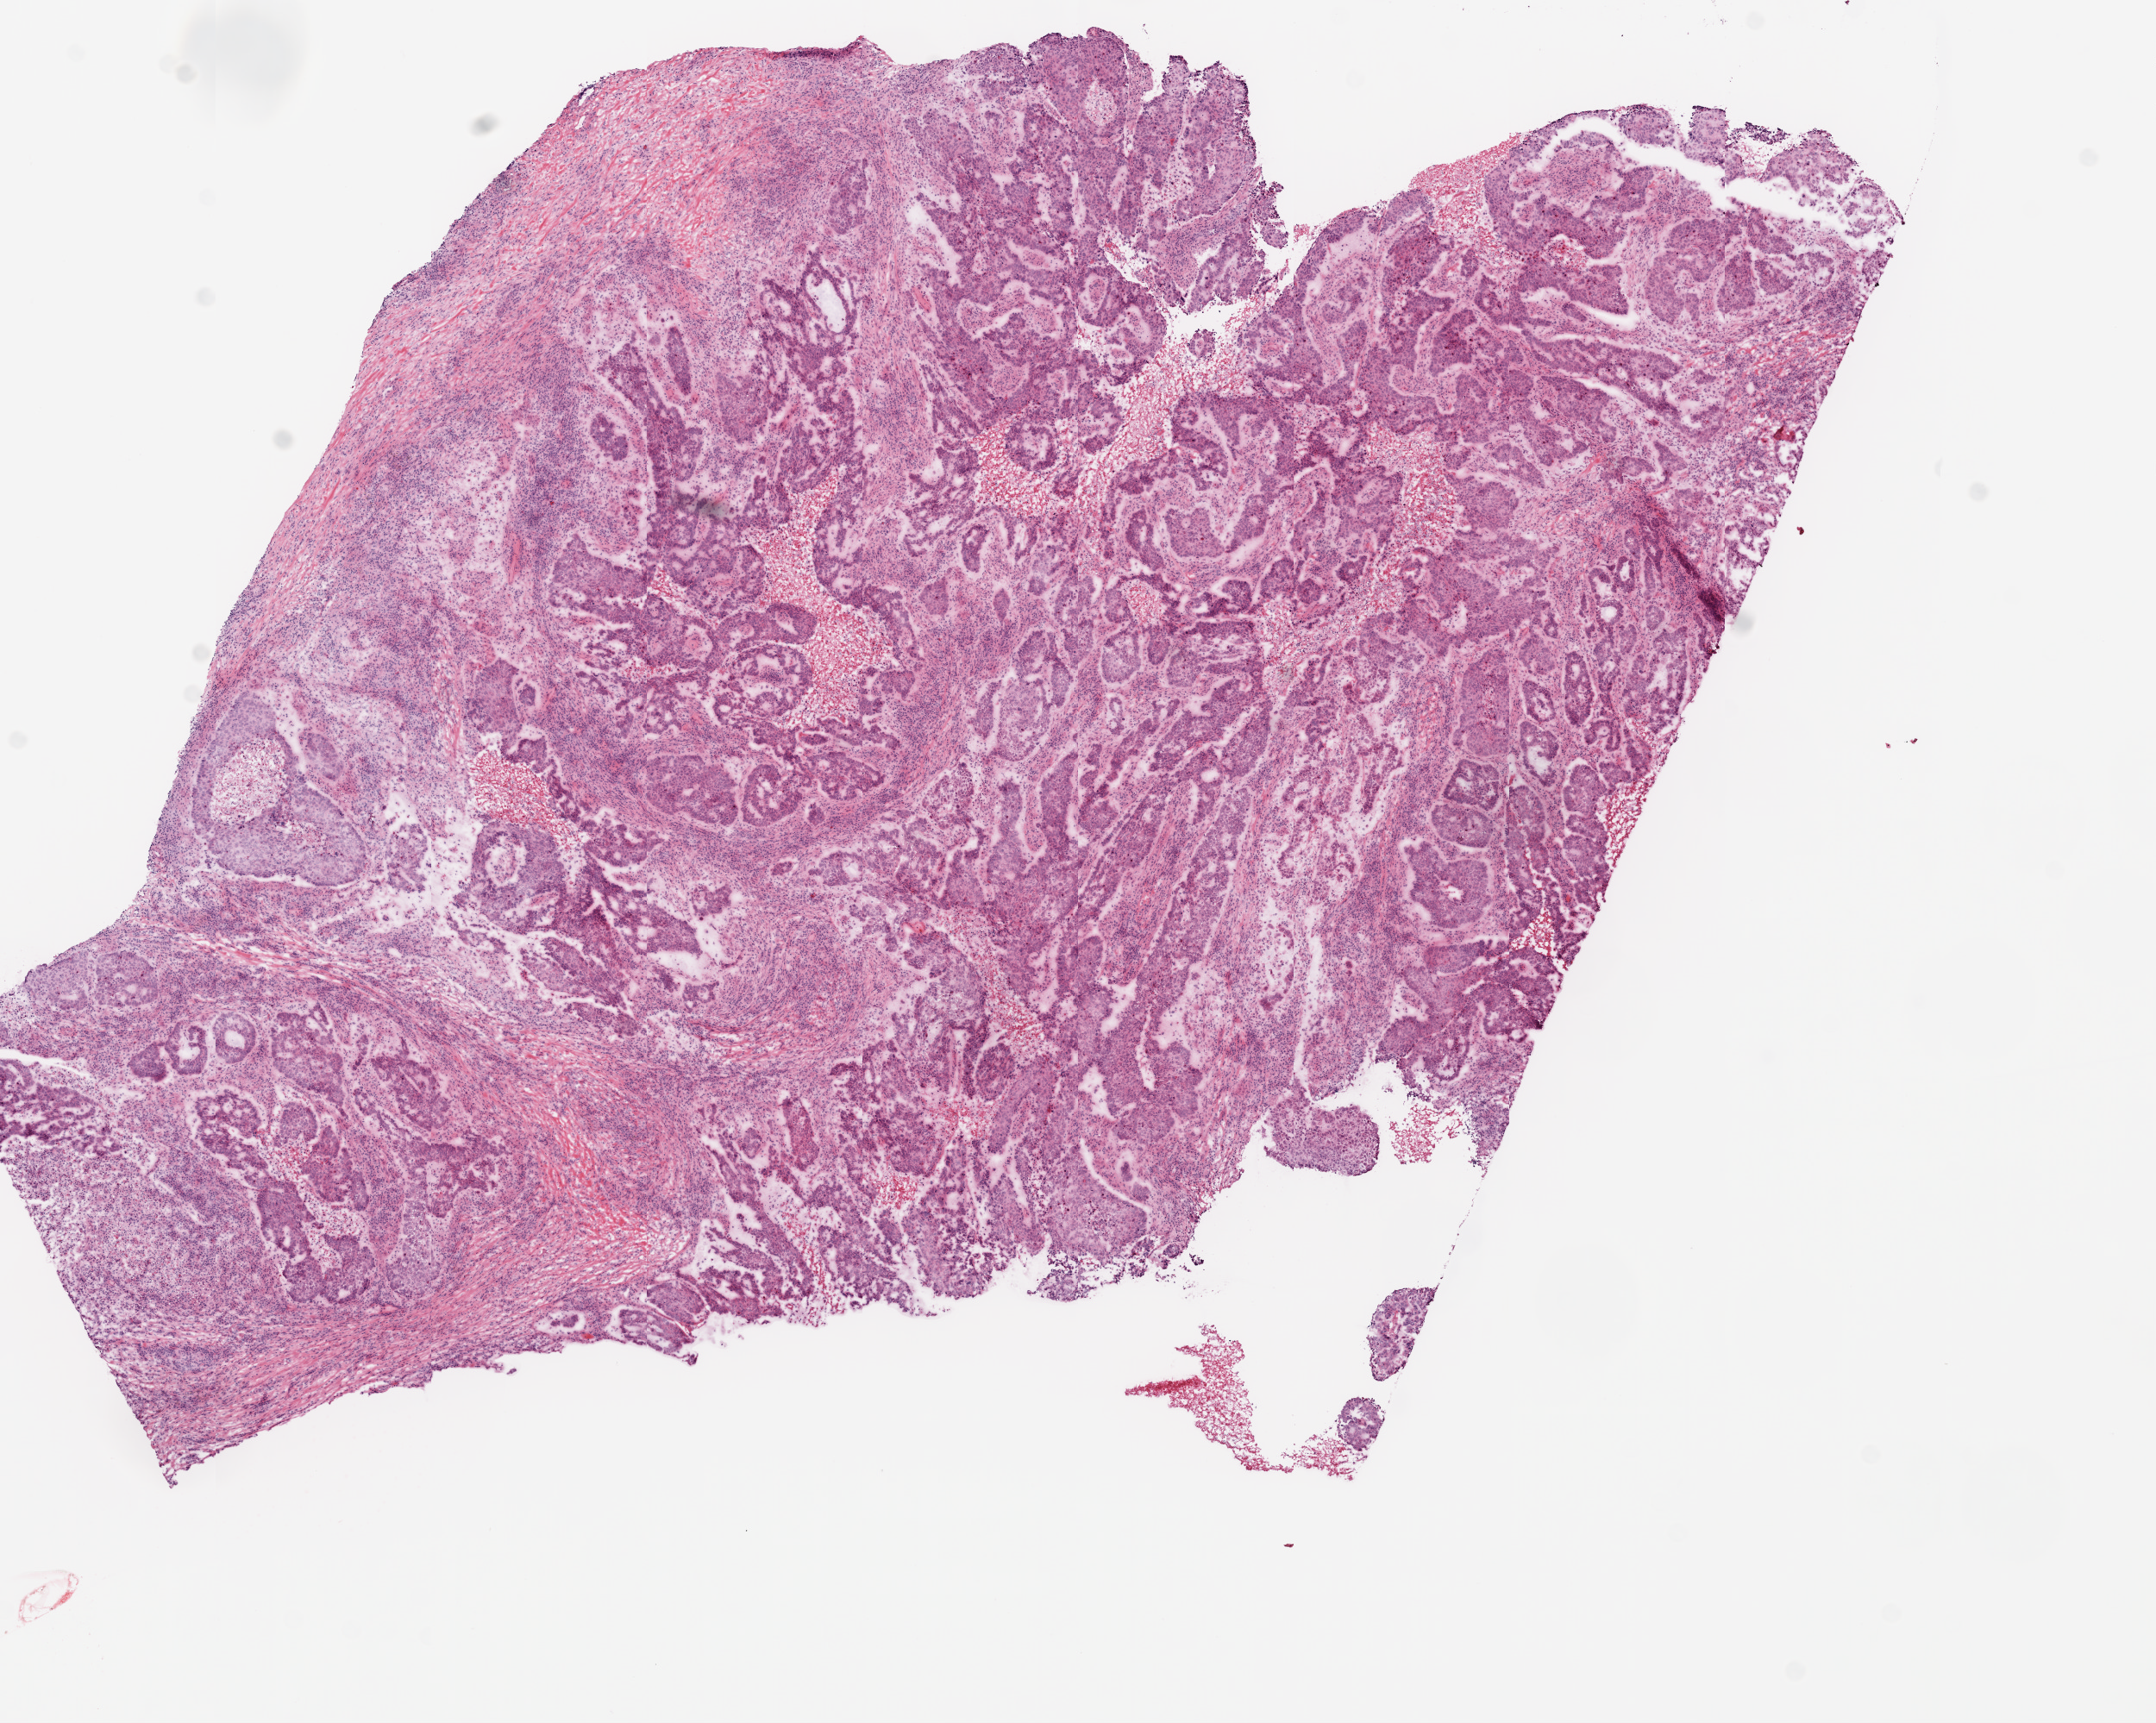
Digitized H&E-stained tissue section (whole slide), whole scanned area (about 10.0 x 8.0 mm) shown as a low-resolution overview, frozen section from the top of the tissue portion, sample: primary tumour, lung. Female patient; age at initial diagnosis 73 years. Pathologist review of this section (percent, as recorded): tumour cells 70%, tumour nuclei 60%, normal cells 0%, stromal cells 20%, necrosis 10%.
AJCC pathologic stage: IB. Pathologic diagnosis: Squamous cell carcinoma, NOS (overlapping lesion of lung). TNM: T2a N0 M0.